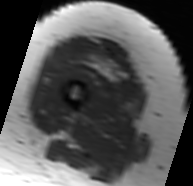
MRI of an extremity soft-tissue mass, one axial slice. Slice 20 of 91 in the series (ordered by position). MR volume resampled by the dataset authors to the PET/CT grid (not the native acquisition matrix). 3.27 mm slice thickness. 193 × 186 image matrix, field of view 188 × 182 mm. Female patient. Case-level facts recorded for this patient, not image findings: histological type: malignant solitary fibrous tumor; grade: intermediate; site of the primary tumour: right thigh.
Outlined on this slice (expert contour drawn on MRI and transferred to this co-registered scan by the dataset authors):
- gross tumour volume including surrounding oedema: bounding box <65,37,130,84> (left, top, right, bottom; pixels)